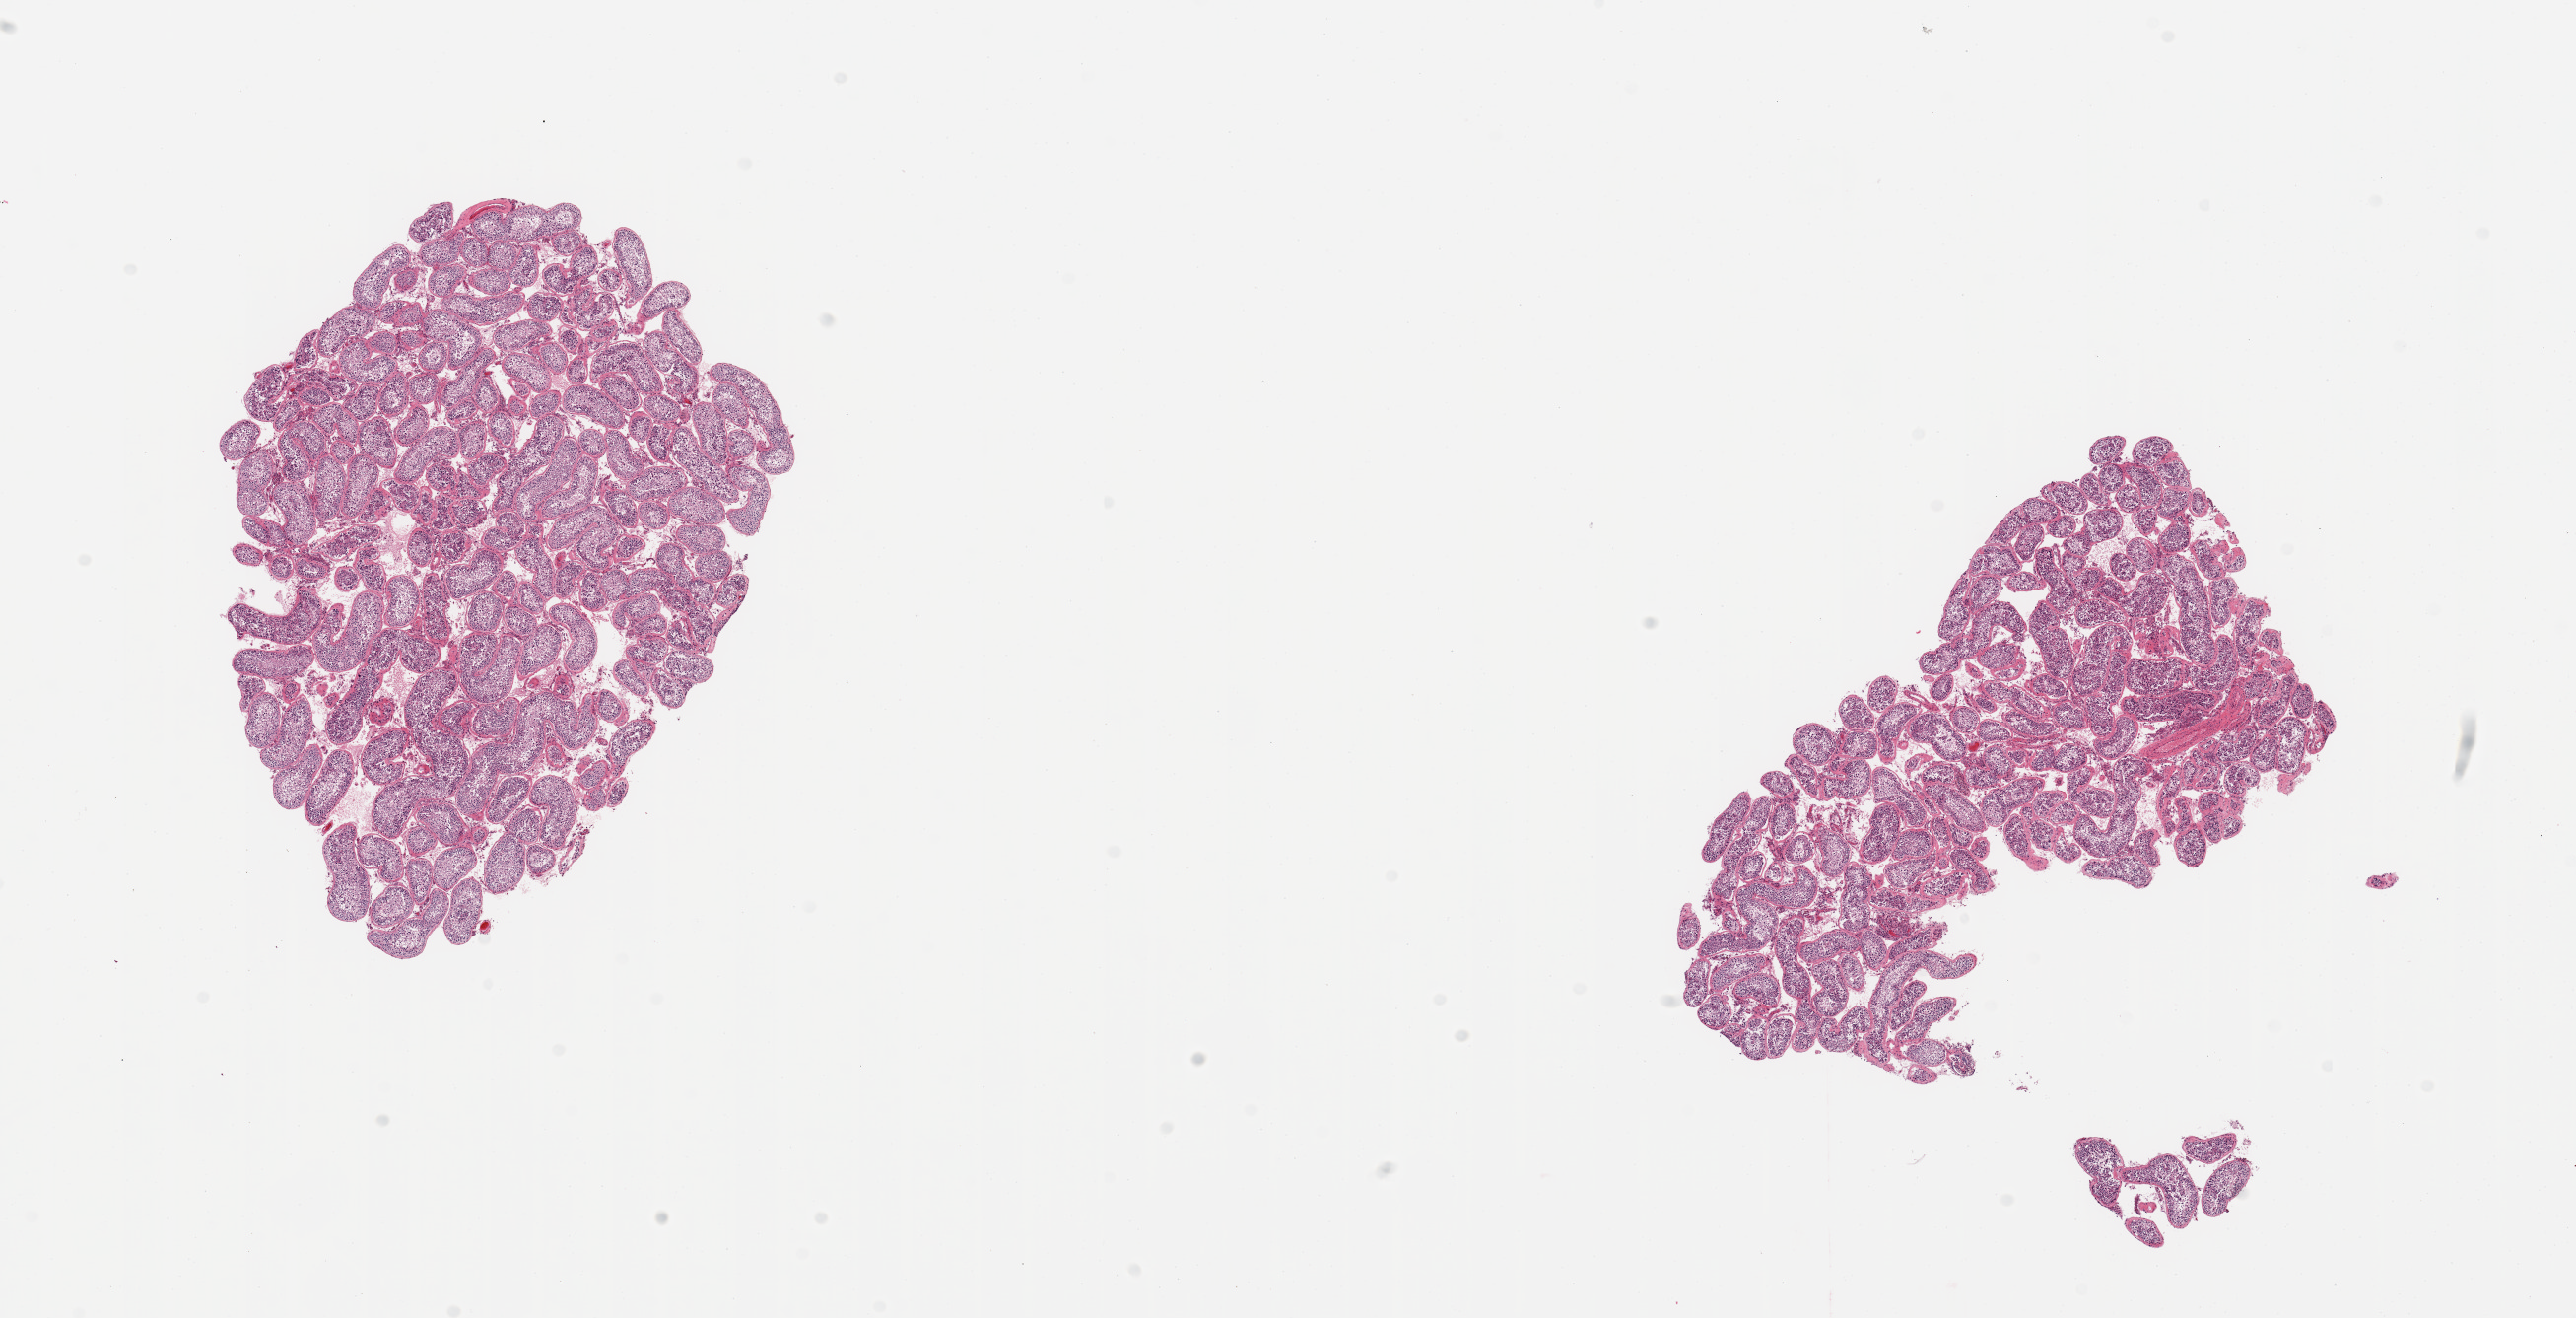
Whole-slide image, hematoxylin and eosin (H&E) stain, whole scanned area (about 20.7 x 10.6 mm, slide scanned at 20x) shown as a low-resolution overview; PAXgene-fixed paraffin-embedded (PFPE) section; section of testis (target tissue); donor tissue sample. Donor: male.
Pathologist's review note for this sample: 2 pieces, spermatogenesis is present.